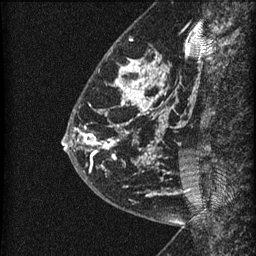
Breast MRI (dynamic contrast-enhanced), one sagittal slice; dynamic contrast-enhanced series, image 2 of 3 at this slice position (ordered by acquisition); 1.5 T; TE 4.2 ms, TR 22.7 ms; 1.5 mm slice thickness; 256 × 256 image matrix. Patient: female, 48 years. From the clinical record (not read from this slice): setting: breast cancer imaged before/during neoadjuvant chemotherapy; receptor status: triple-negative.
Outlined on this slice (semi-automatic segmentation, software-assisted and operator-edited):
- analysis volume of interest (the breast-tissue region the enhancement analysis was run in; not a lesion): box from (x=81, y=23) to (x=186, y=202) px
- tumour enhancement mask (voxels above the 90 % enhancement threshold inside the analysis volume of interest): (x=81, y=62)–(x=161, y=195)